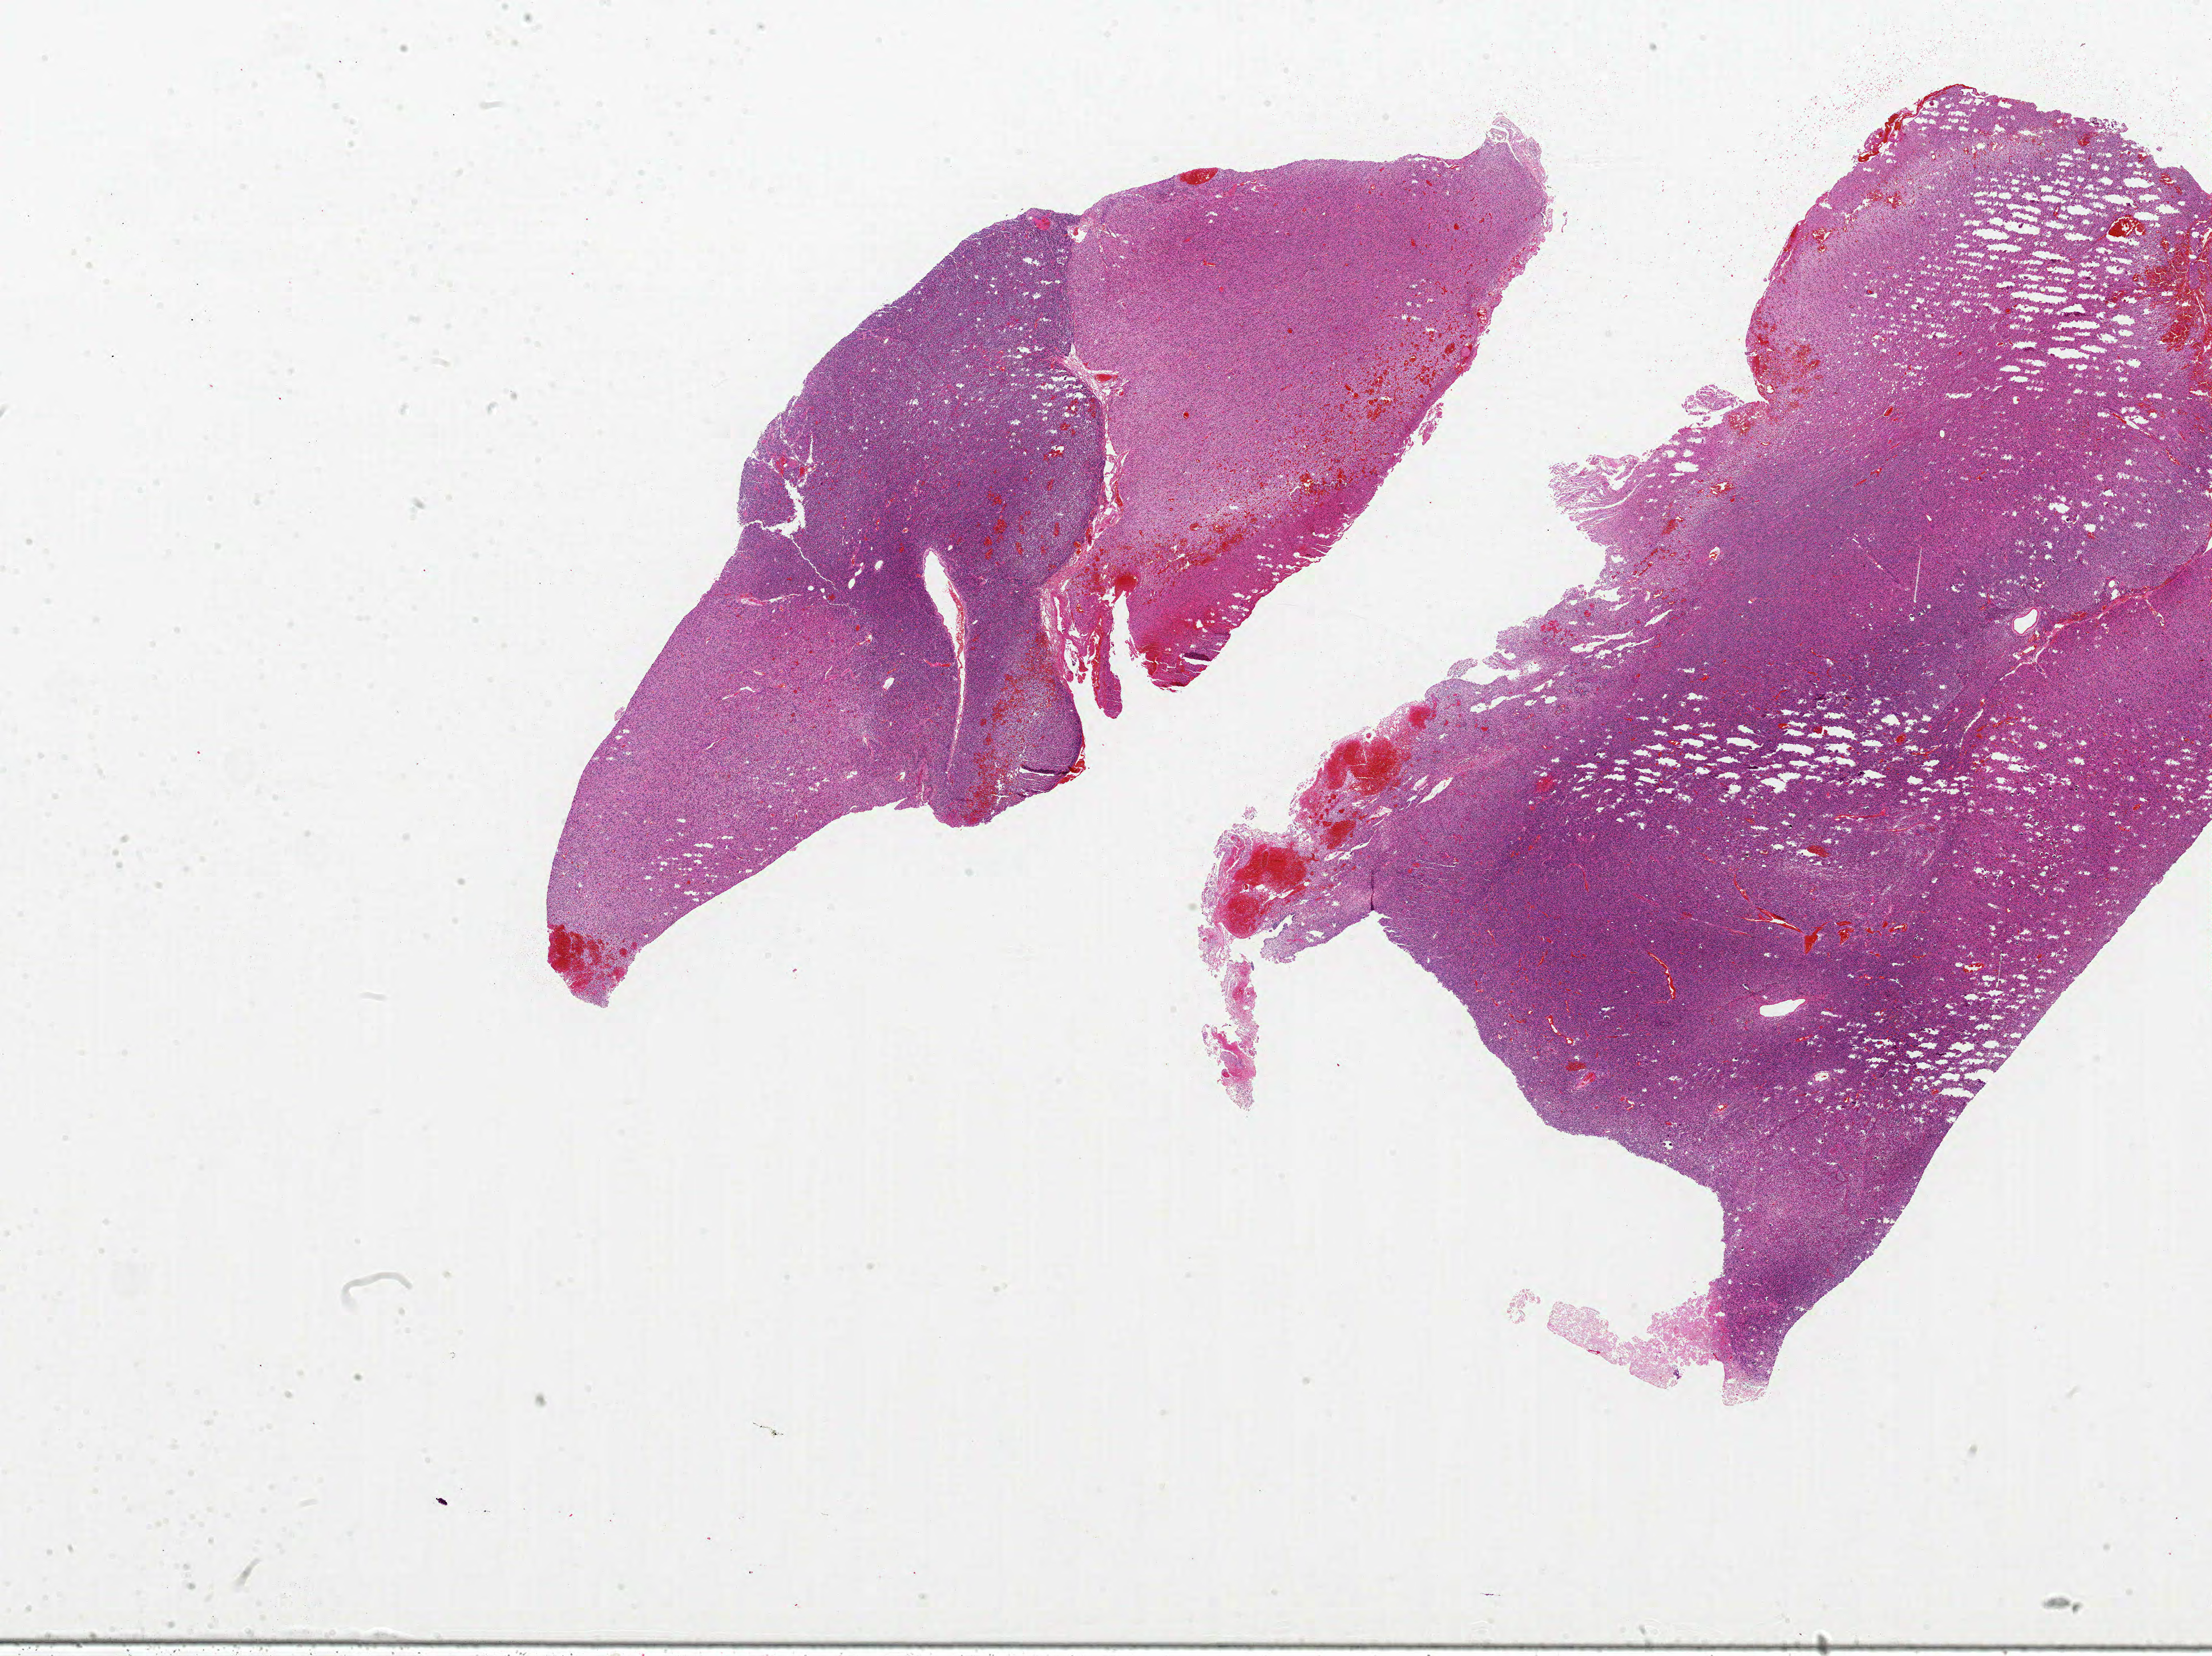
H&E-stained whole-slide image — a low-resolution overview of the entire scanned area, about 31.0 x 23.2 mm (slide scanned at 20x). Formalin-fixed paraffin-embedded (FFPE) diagnostic section. Brain, primary tumour sample. Male patient; age at initial diagnosis 60 years.
Diagnosis: Glioblastoma.